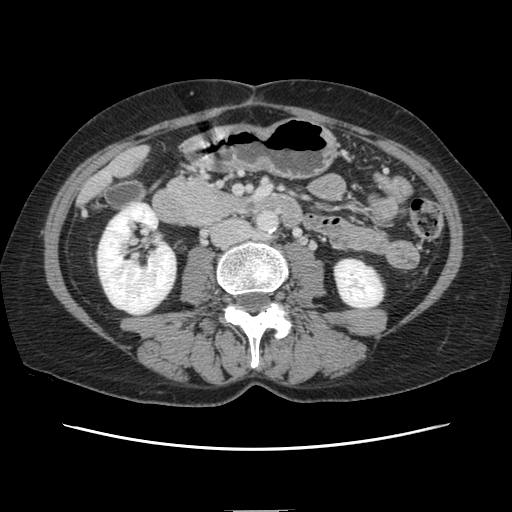
Contrast-enhanced abdominal CT, one axial slice. Position 28 of 141 along the scan axis. 120 kVp. Intravenous contrast given. Soft-tissue window (W 400 / L 40 HU). 2.5 mm slice thickness. 512 × 512 image matrix, field of view 350 × 350 mm. Female patient, age 63 years. Case-level facts recorded for this patient, not image findings: diagnosis: colorectal cancer liver metastases, imaged before liver resection; multiple liver metastases: yes; largest metastasis: 3.2 cm; disease in both lobes: yes.
Structures marked on this image (manually delineated by an expert):
- liver: bounding box (x1, y1, x2, y2) in pixels: (83, 148, 146, 199)